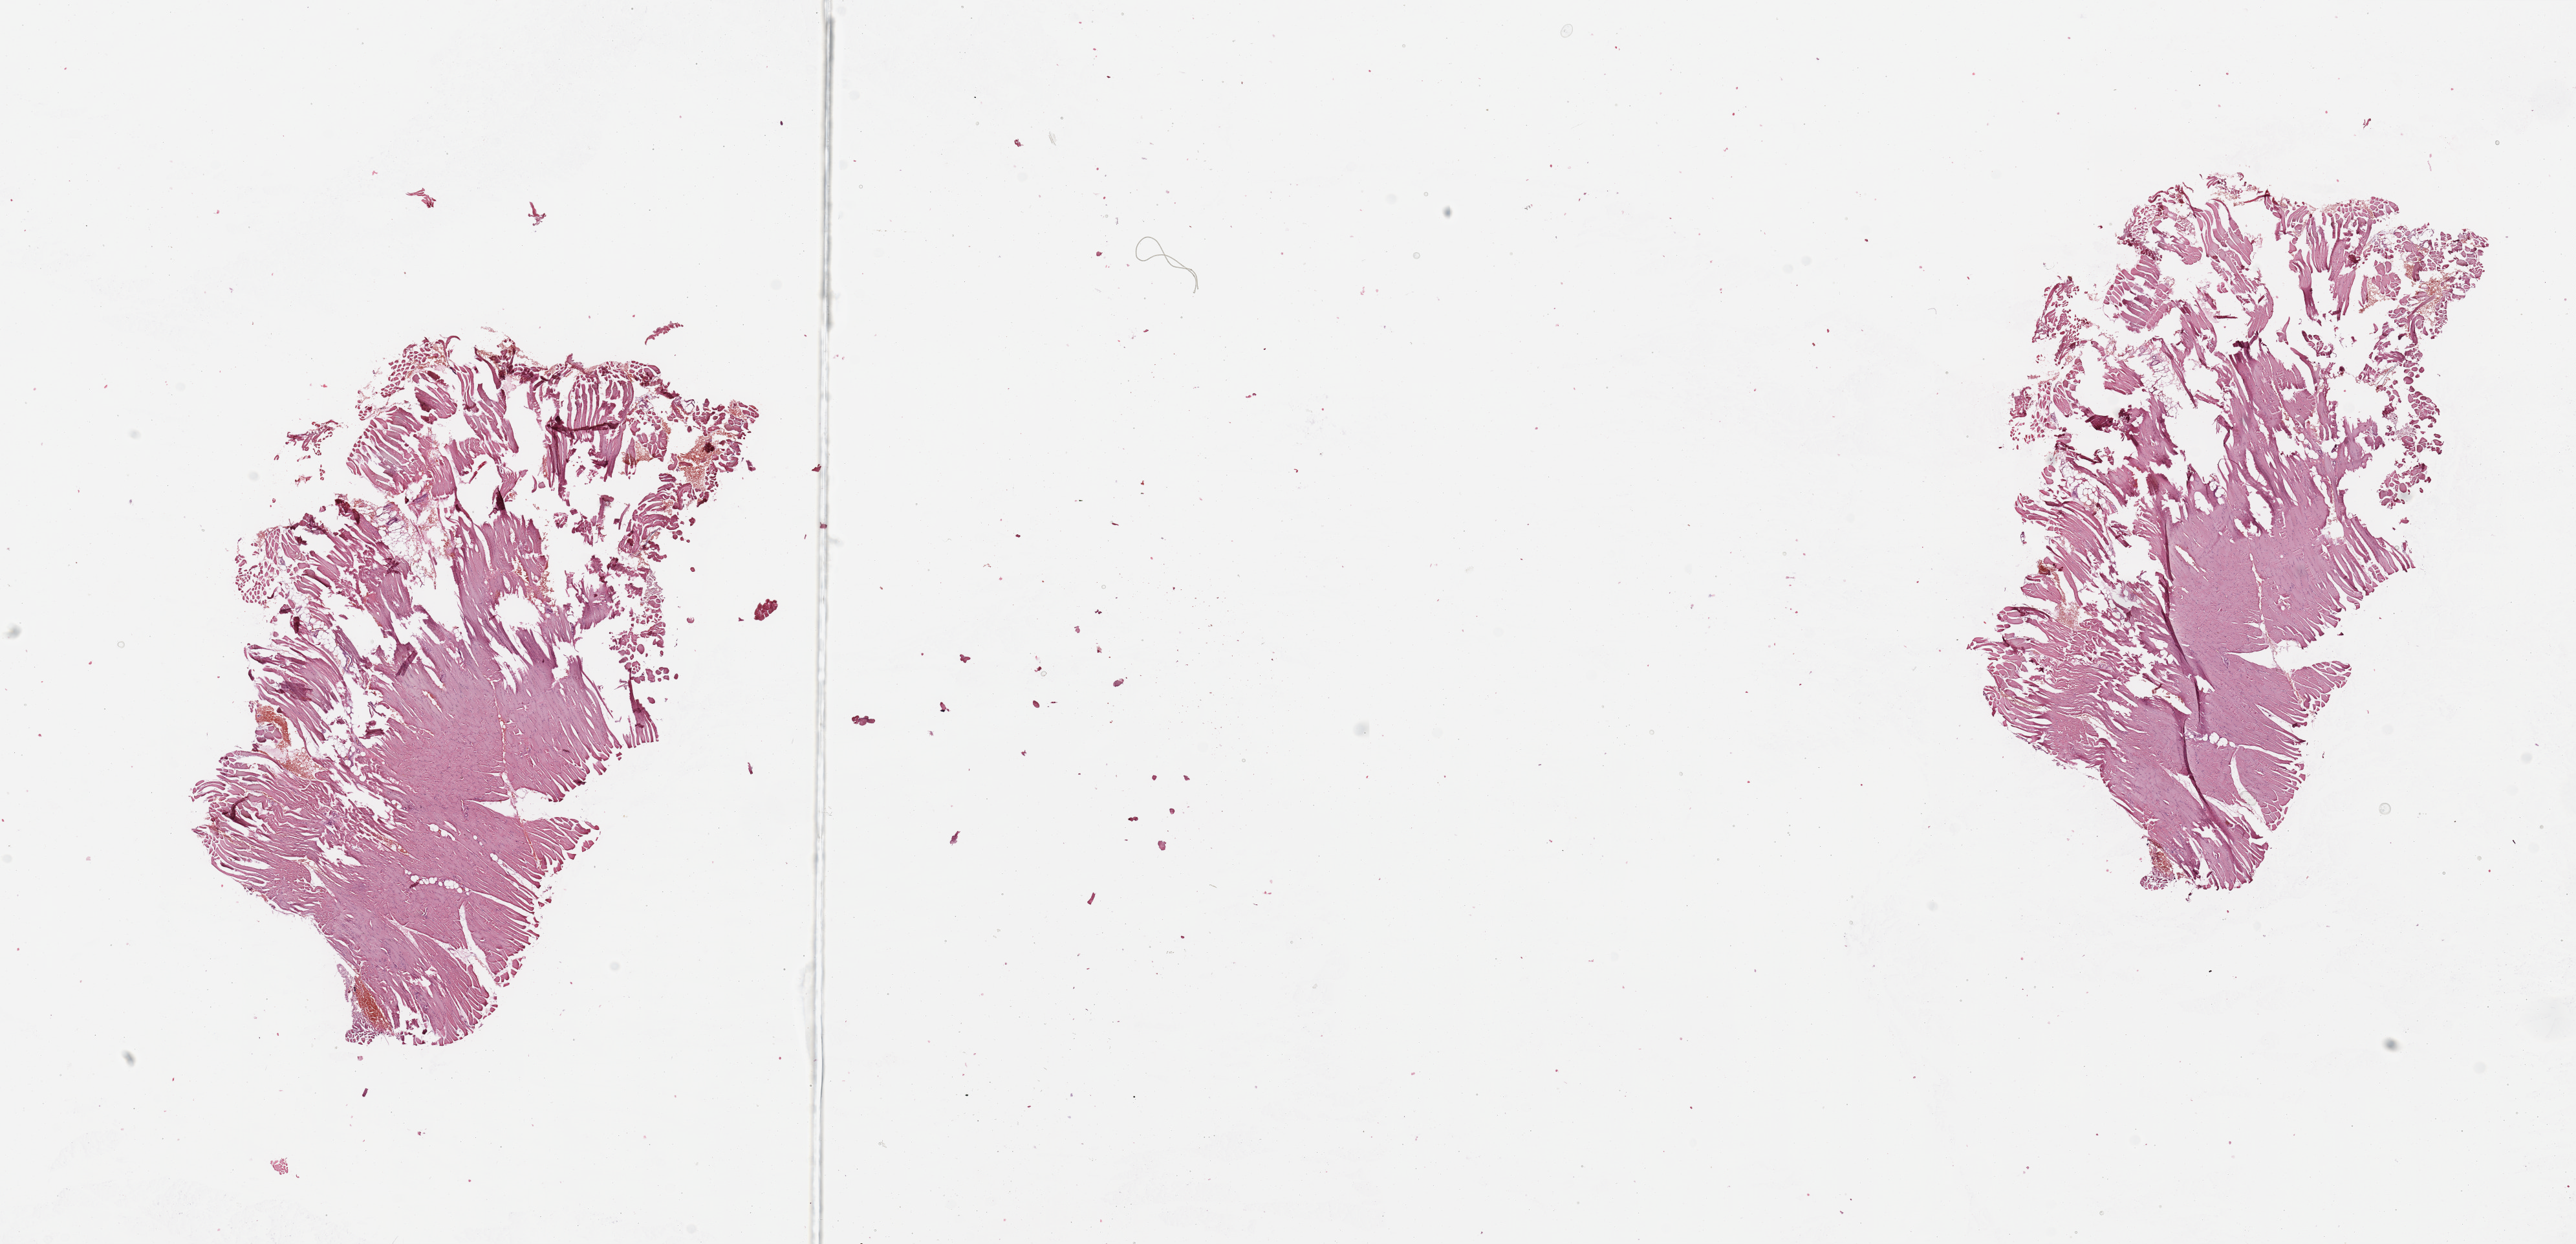
Whole-slide histology image, H&E — shown as a low-resolution overview of the whole scanned area (about 31.5 x 15.2 mm, slide scanned at 20x); normal (non-tumour) tissue sample. Patient: female, age 52 years.
- this section: normal (non-tumour) tissue from the same patient
- patient diagnosis (cohort enrolment): sarcoma (site not recorded at cohort level)